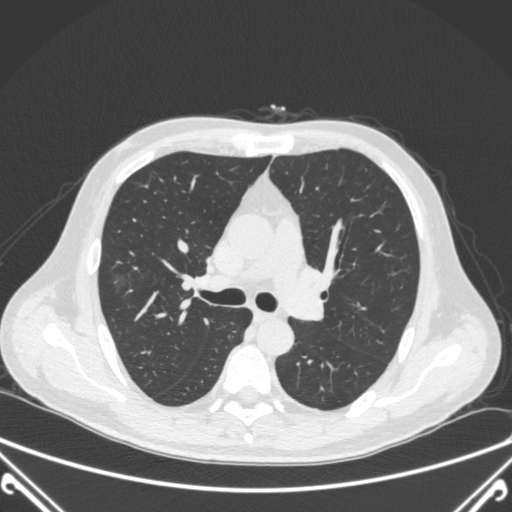
Chest CT, one axial slice. Position 231 of 360 along the scan axis. 120 kVp. Lung window (W 1500 / L -600 HU). 1 mm slice thickness. 512 × 512 image matrix, field of view 380 × 380 mm. Male patient, age 64 years. From the clinical record (not read from this slice): clinical TNM (as recorded): T1c N0 M0; histopathological grade: G2.
Outlined on this slice (bounding box drawn by a radiologist):
- lung tumour (recorded histology: adenocarcinoma): bounding box (x1, y1, x2, y2) in pixels: (103, 270, 134, 298)